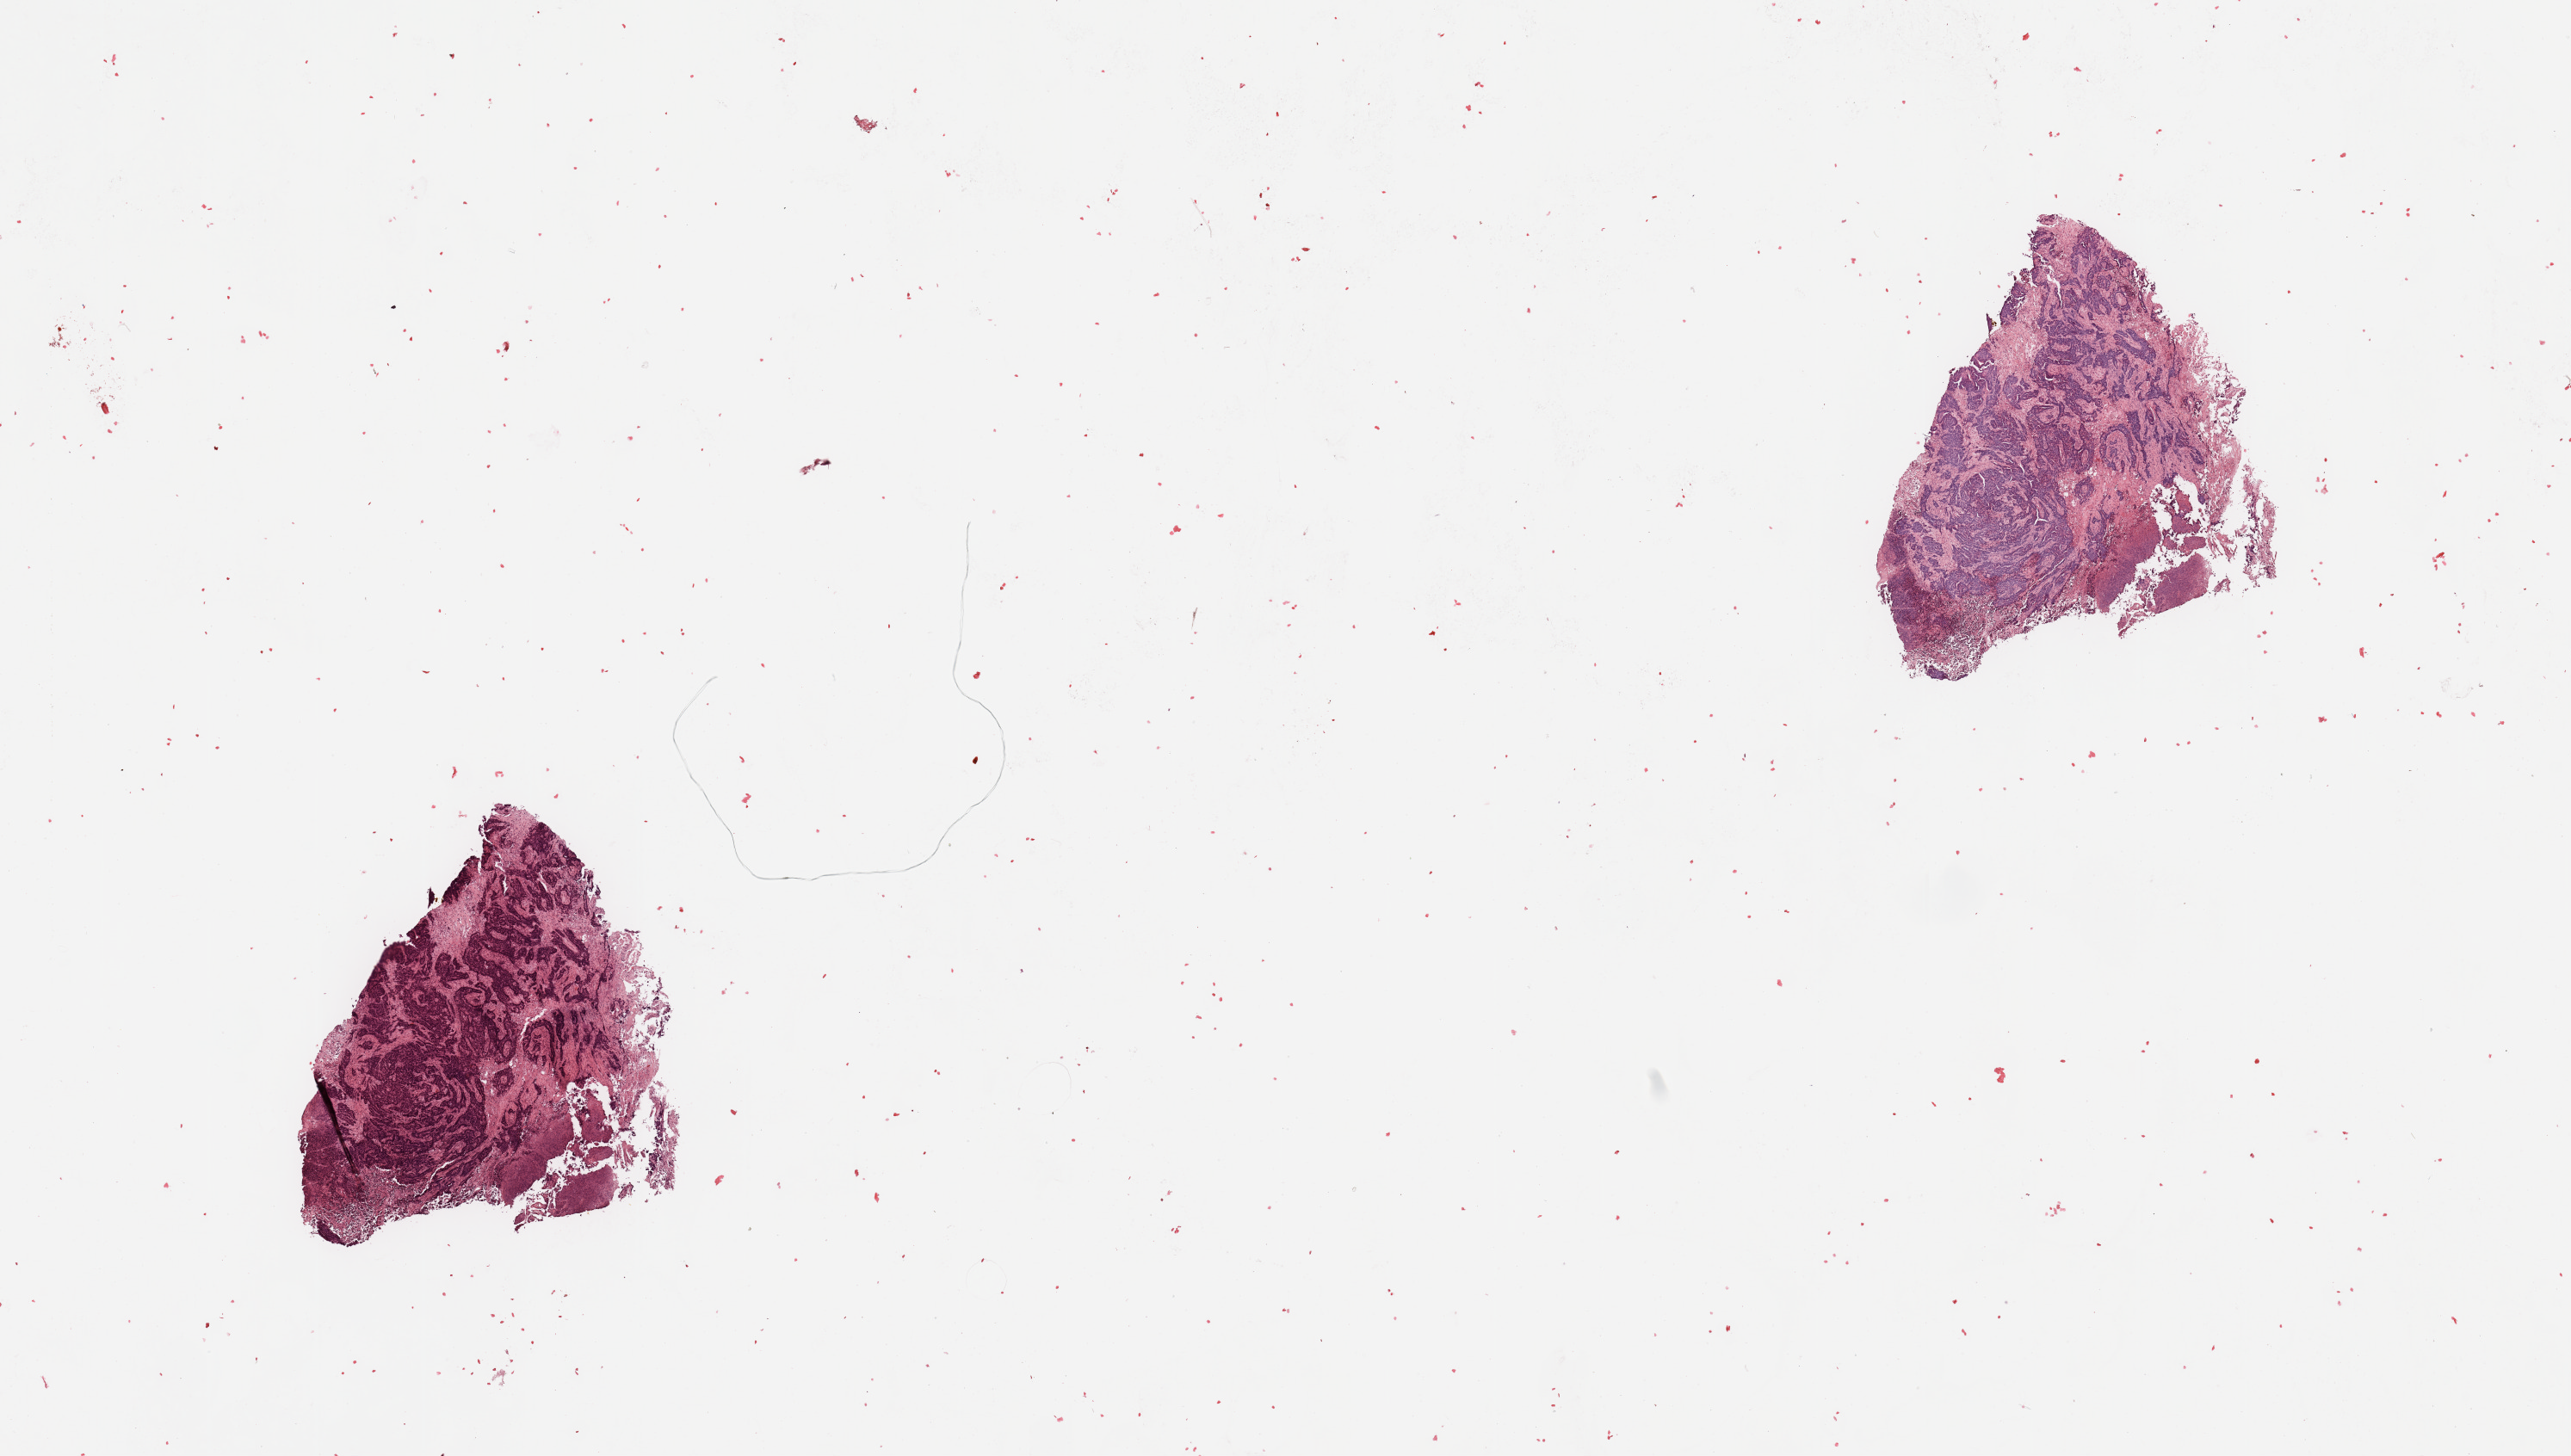
H&E-stained whole-slide image, whole scanned area (about 23.6 x 13.4 mm) shown as a low-resolution overview, tumour tissue sample, uterus. 77-year-old female patient. Histologic grade: G3 (poorly differentiated).
Primary tumour site (as recorded): anterior endometrium. AJCC pathologic stage: I. Histologic diagnosis: Endometrioid adenocarcinoma, NOS.